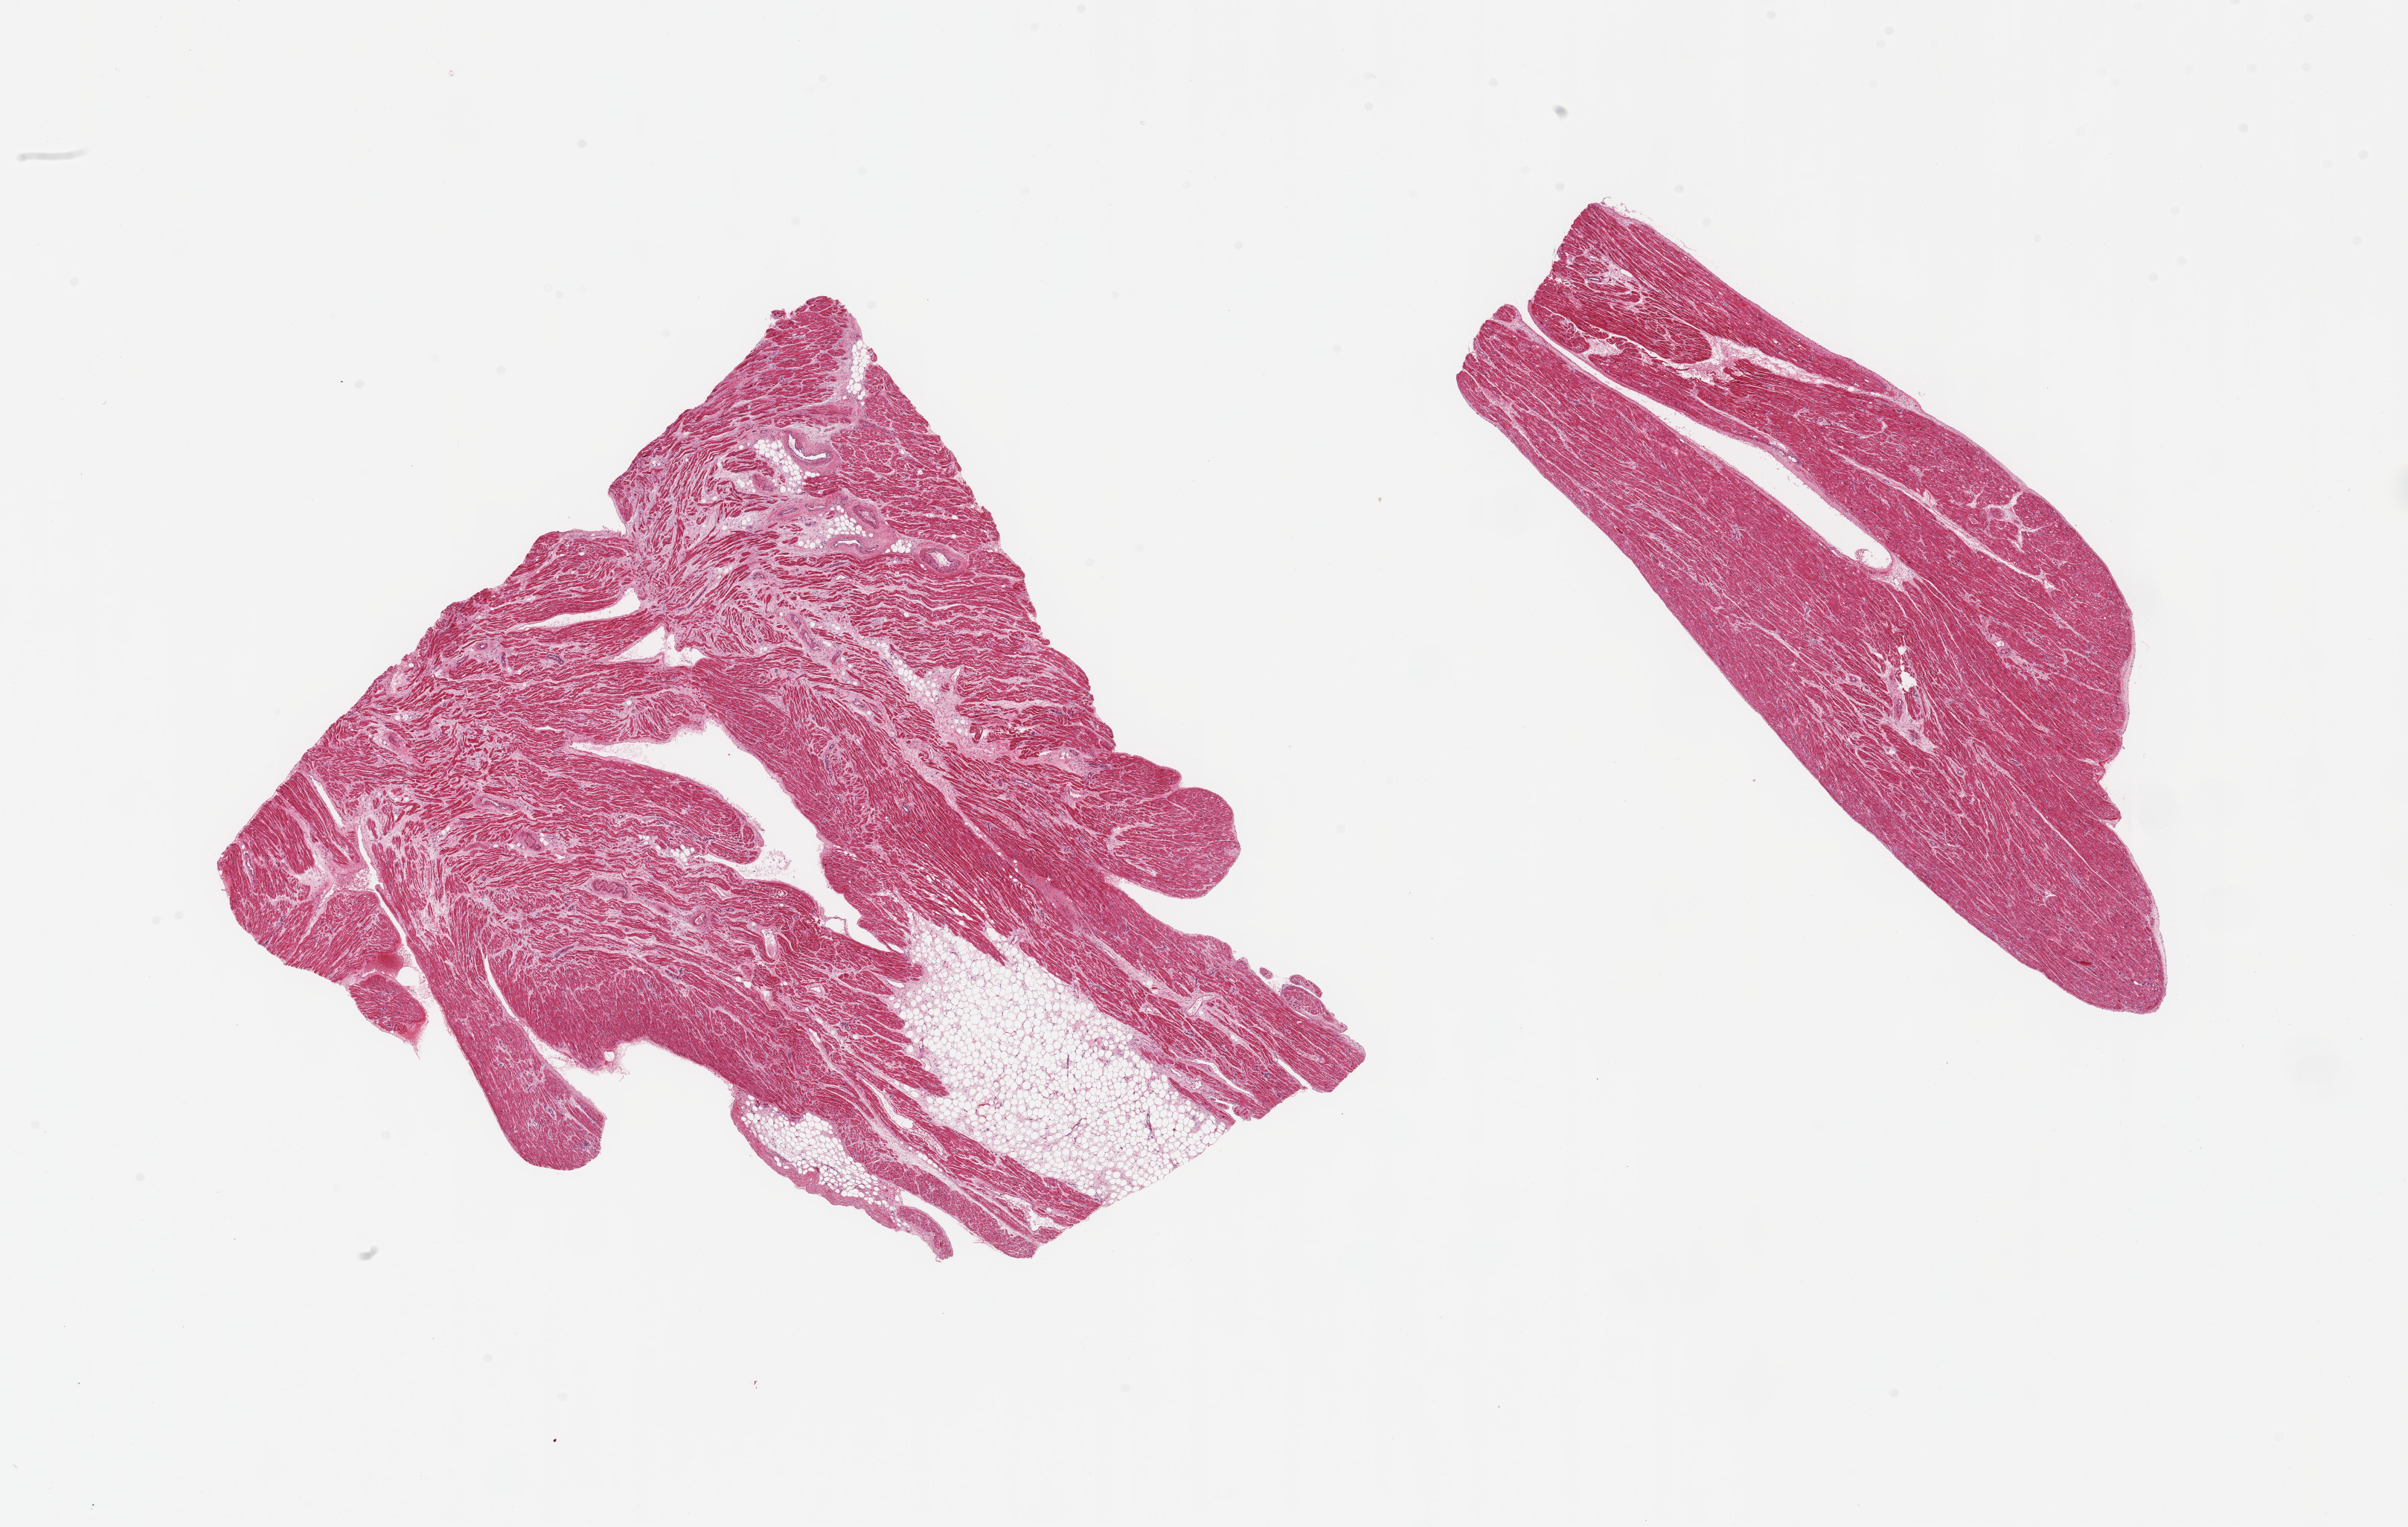
Digitized H&E-stained section, brightfield, shown as a low-resolution overview of the whole scanned area (about 25.6 x 16.2 mm), PAXgene-fixed paraffin-embedded (PFPE) section, sampled site (target tissue): auricular appendage, tissue donor sample. Donor sex: male.
* reviewer comment on this tissue sample: 2 pieces; 1 pure muscle; other with 20% fat content